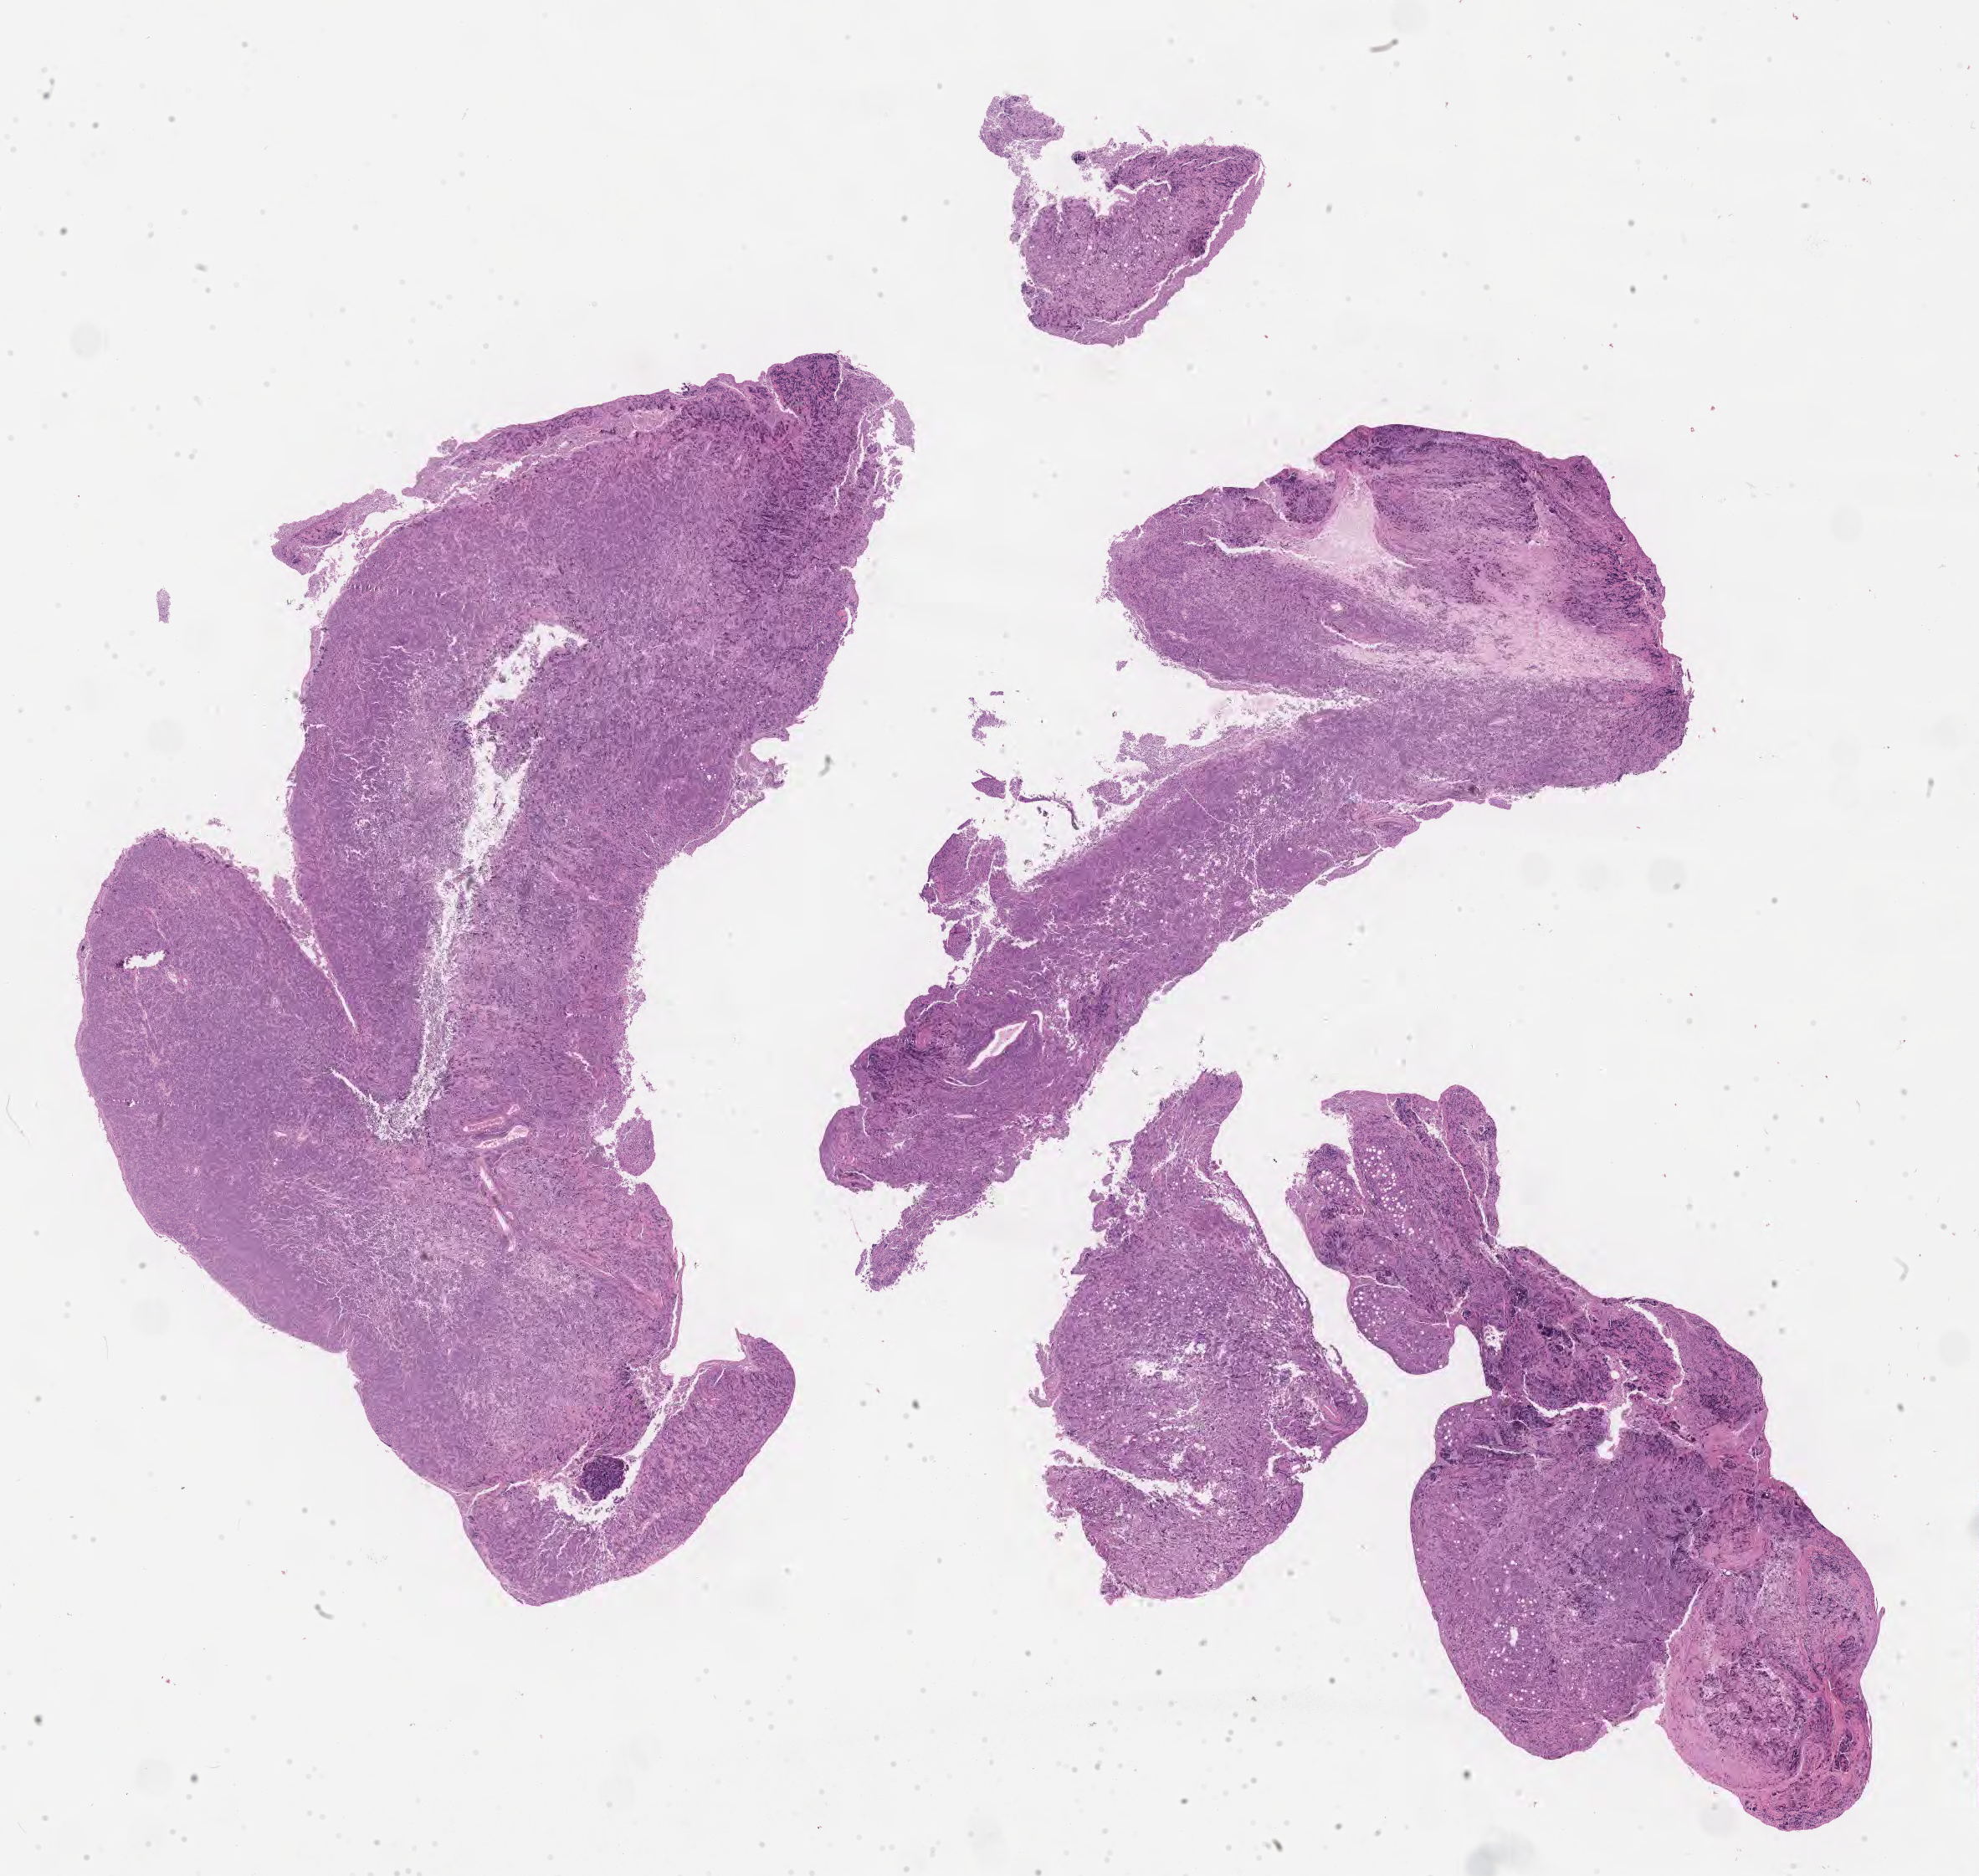
Digitized hematoxylin and eosin (H&E)-stained section — low-resolution overview of the scanned area, about 19.1 x 18.1 mm; tumor tissue; site: abdomen proper. Male patient; age at initial diagnosis 5 years.
* diagnosis: Burkitt lymphoma, NOS